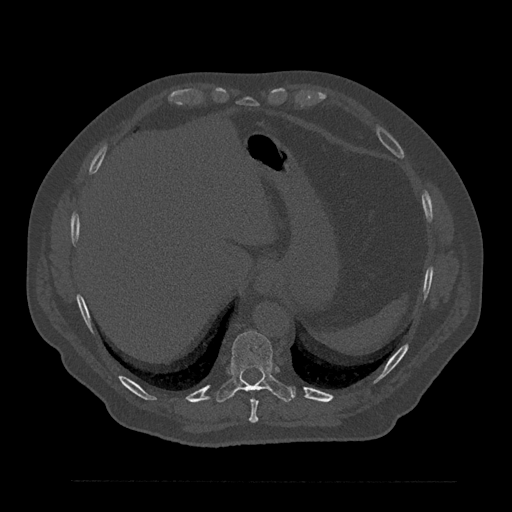
CT including the spine, one axial slice; slice 363 of 797 in the series (ordered by position); reconstruction kernel Br40s/3; bone window (W 1800 / L 400 HU); 512 × 512 image matrix, field of view 430 × 430 mm. Patient: male, 61 years. From the clinical record (not read from this slice): primary cancer: prostate.
Outlined on this slice (semi-automatic segmentation, software-assisted and operator-edited):
- T10 vertebra: bounding box (x1, y1, x2, y2) in pixels: (216, 331, 295, 403)
- T9 vertebra: (249, 399, 258, 423)